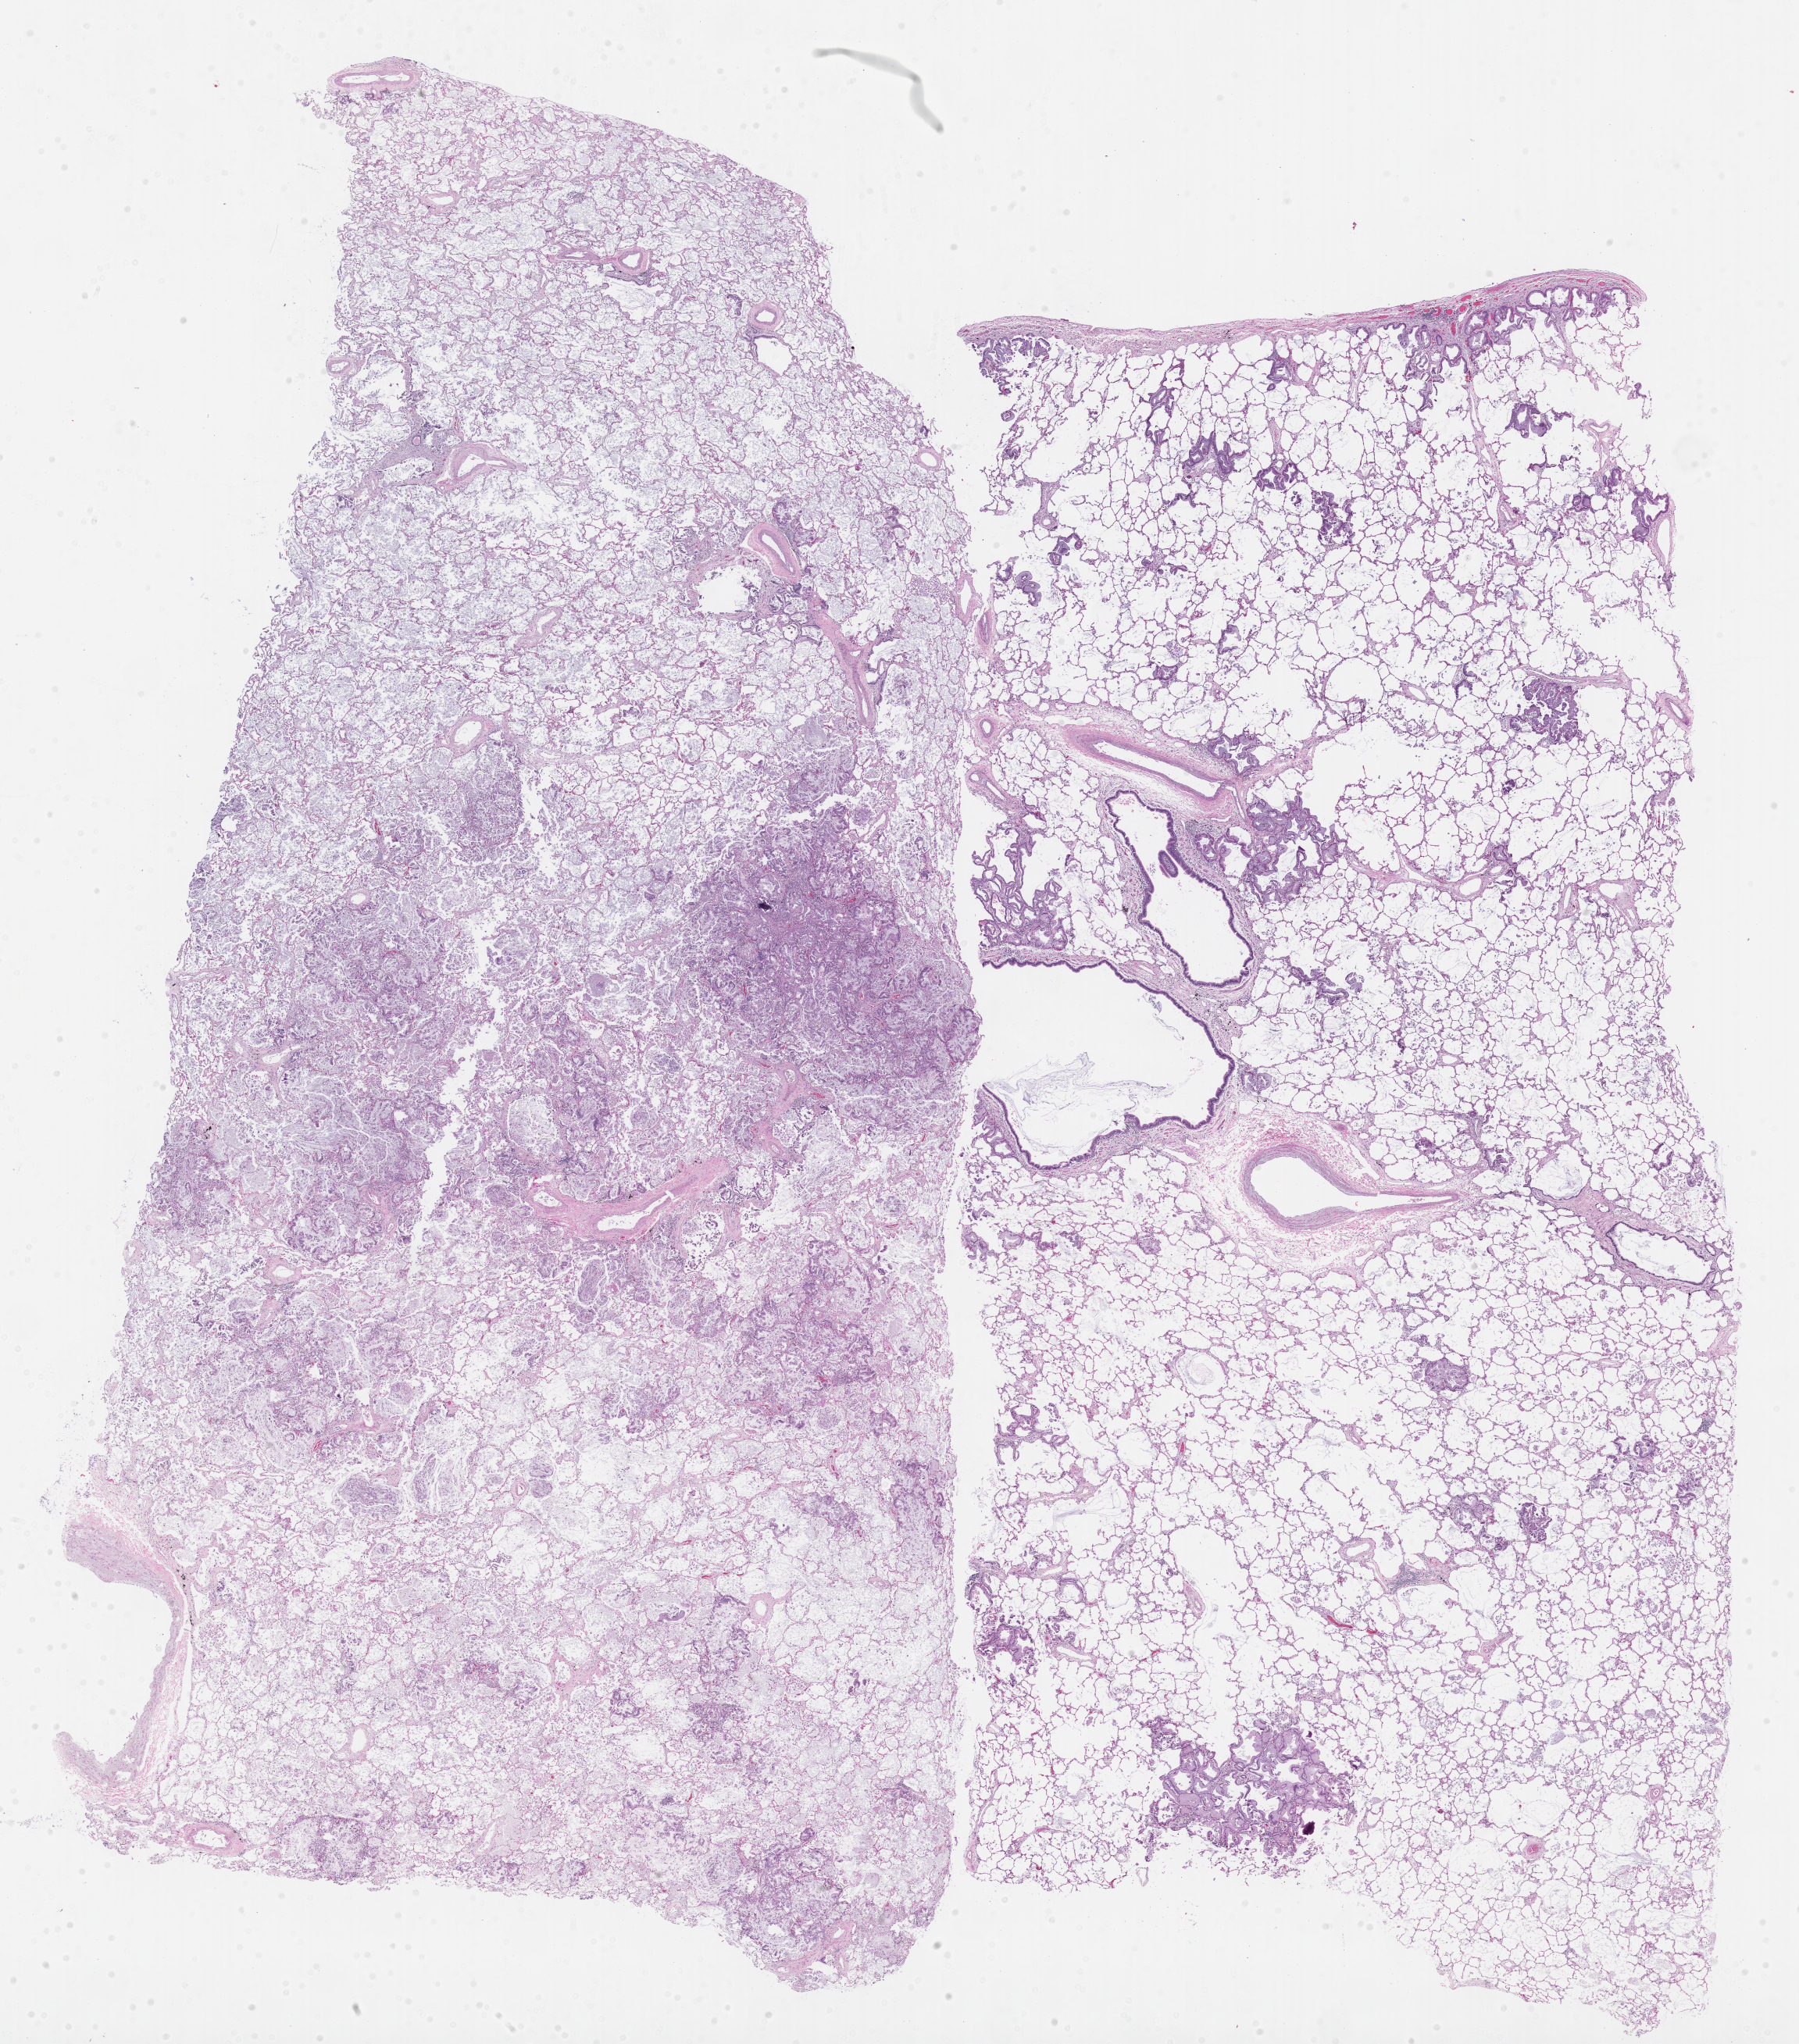
Hematoxylin and eosin (H&E) whole-slide image, whole scanned area (about 18.6 x 21.1 mm) shown as a low-resolution overview. FFPE section. Primary tumor. Site: lower lobe of left lung. Male, age 76 years at initial diagnosis. Tumor grade: G1 (well differentiated). Pathologist review of this section (percent, as recorded): tumor cells 10%, tumor nuclei 10%, stromal cells 0%, necrosis 0%, normal cells 90%. Inflammatory infiltration, as recorded: lymphocyte infiltration 0%, monocyte infiltration 0%, neutrophil infiltration 0%.
- section: top of the tissue portion
- diagnosis: Adenocarcinoma of lung, mucinous
- AJCC pathologic stage: Stage IIIA